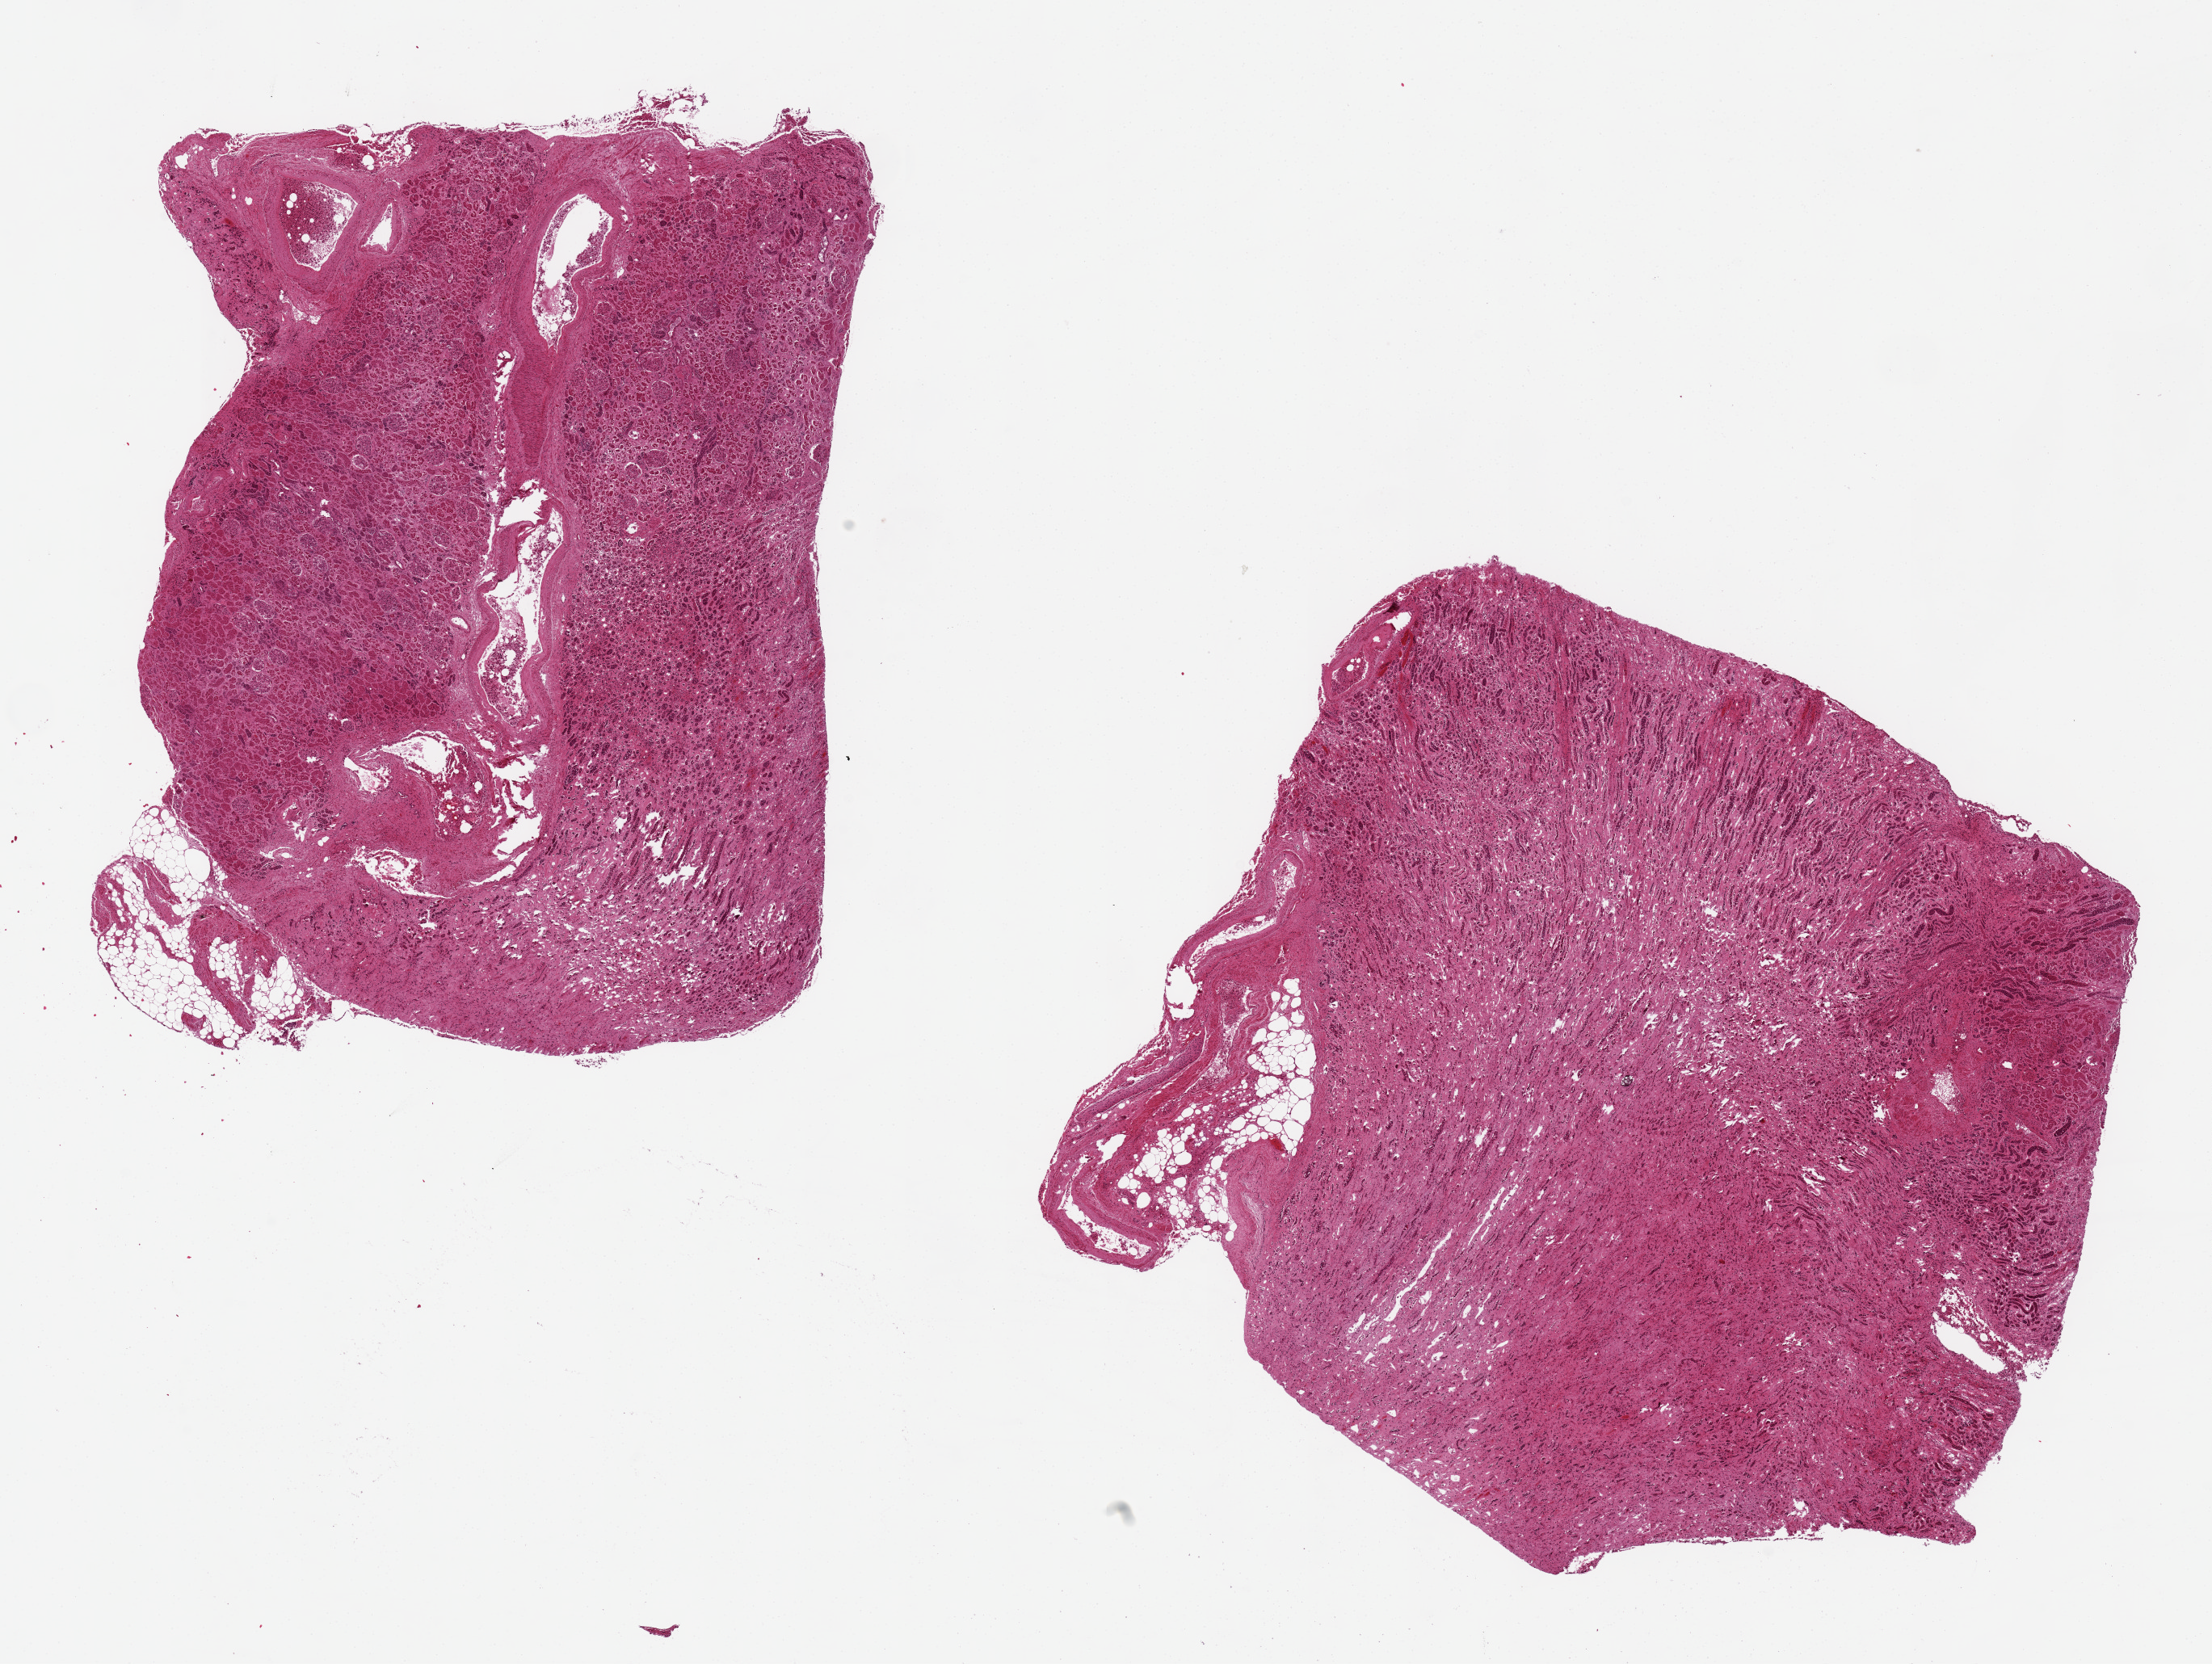
H&E whole-slide image, shown as a low-resolution overview of the whole scanned area (about 21.7 x 16.3 mm, slide scanned at 20x). PAXgene-fixed, paraffin-embedded tissue. Sampled site (target tissue): renal medulla. Donor tissue sample. Female donor.
• pathologist's review note for this sample: 3 aliquosts, one all cortex, one is medulla, cannot be retained as either